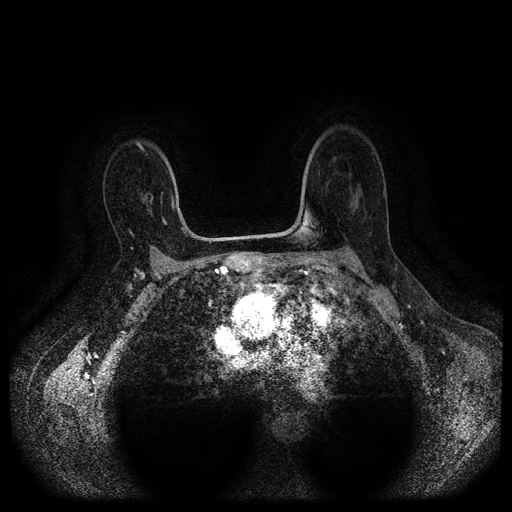
Breast MRI (dynamic contrast-enhanced, multi-phase), one axial slice; position 63 of 112 along the scan axis; dynamic contrast-enhanced series, time point 2 of 5 at this slice position (early post-contrast); 1.5 T; TE 2.6 ms, TR 5.4 ms; 2 mm slice thickness; 512 × 512 image matrix, field of view 340 × 340 mm. Patient: female, 53 years.
Annotated regions visible in this slice (semi-automatically segmented with operator editing):
- breast lesion (labelled 'tumour' in the annotation; benign lesions carry a separate 'benign' label): bounding box (x1, y1, x2, y2) in pixels: (140, 189, 154, 216)